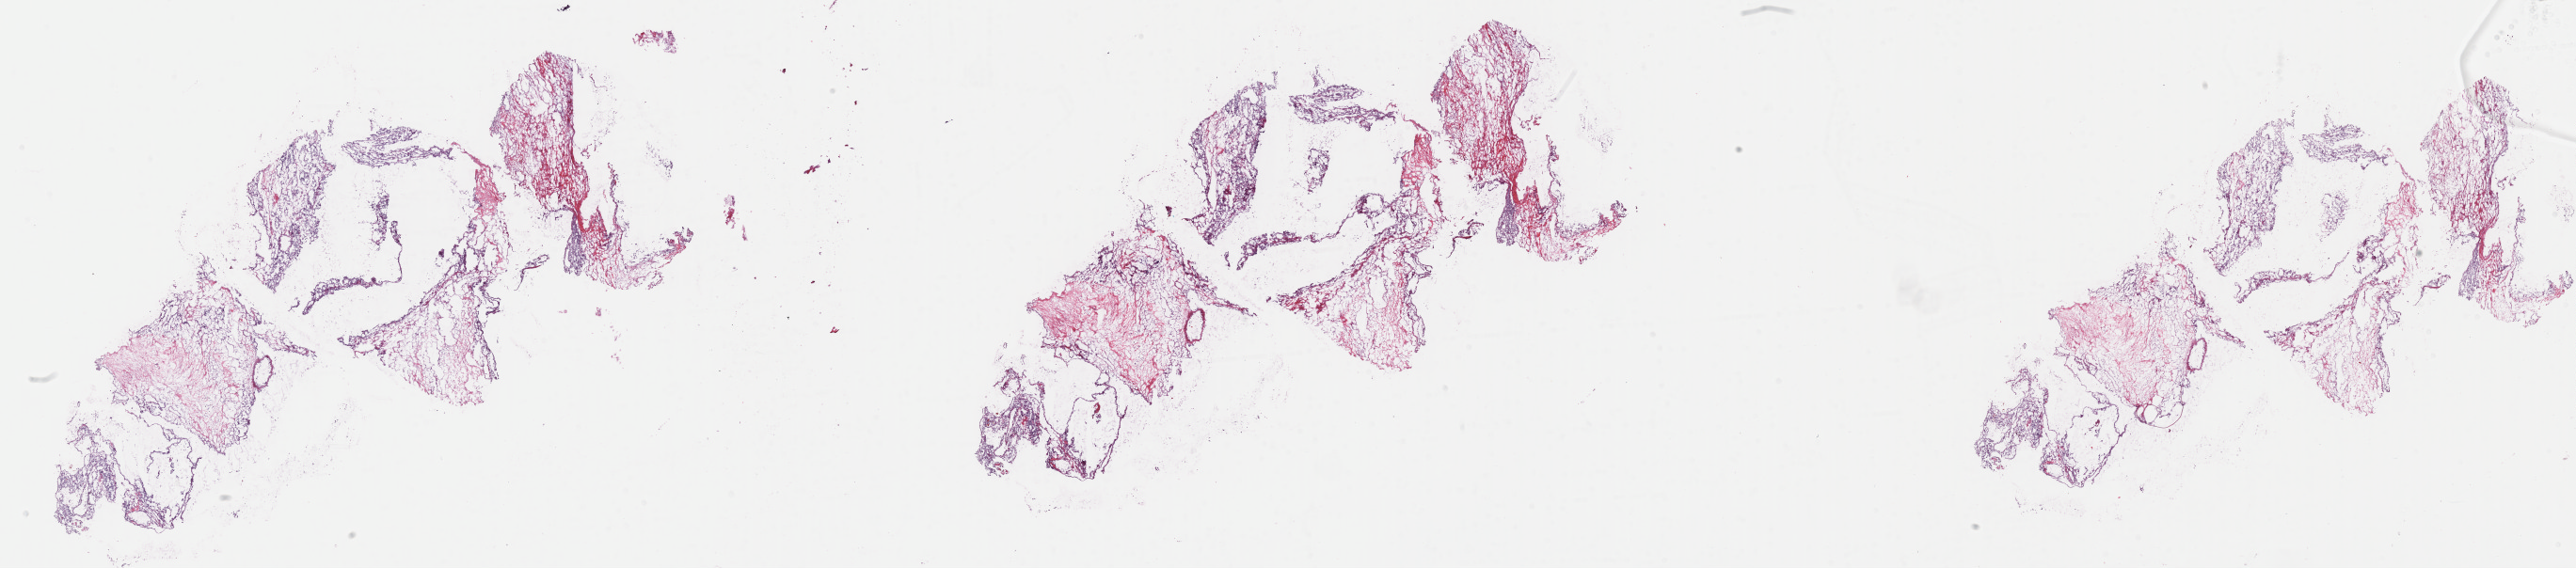
Whole-slide histology image, Hematoxylin and eosin (H&E) stained — a low-resolution overview of the entire scanned area, about 44.3 x 9.8 mm, frozen section, sample: primary tumour, kidney. Male patient; age at initial diagnosis 49 years.
Diagnosis: Papillary adenocarcinoma, NOS.